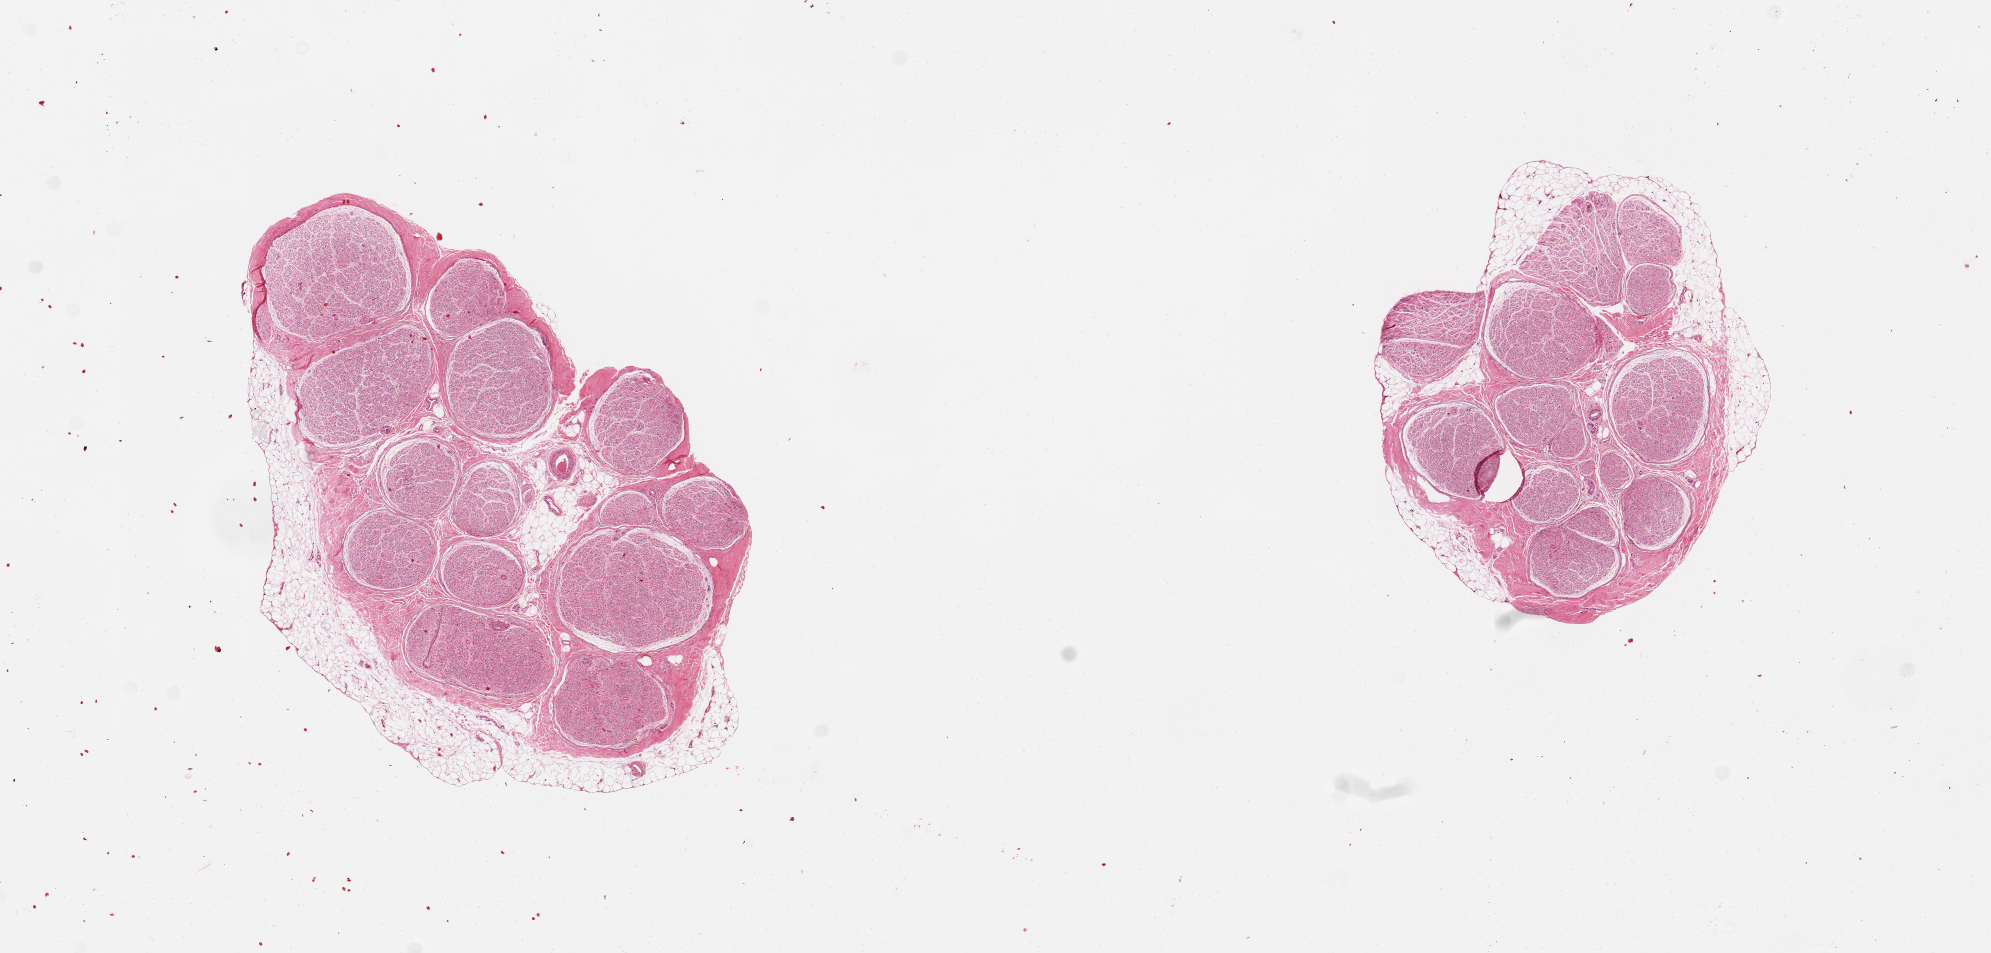
Haematoxylin and eosin whole-slide image, whole scanned area (about 15.8 x 7.5 mm, acquisition: 20x scan) shown as a low-resolution overview. PAXgene-fixed paraffin-embedded (PFPE) section. Target tissue: tibial nerve. Donor tissue sample.
Reviewer comment on this tissue sample: 2 pieces, partial rim adherent fat, ~0.4-0.5mm.